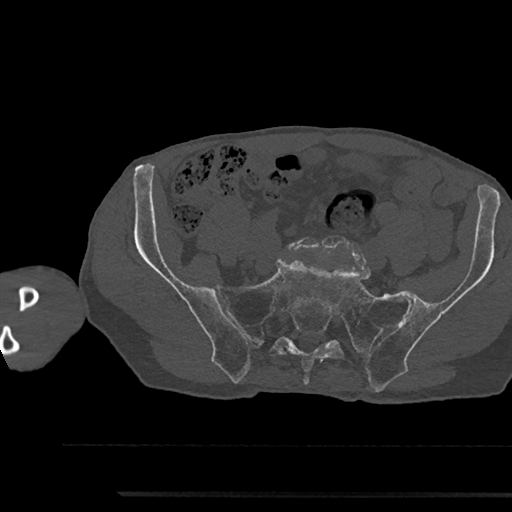
CT including the spine, one axial slice; slice 282 of 797 in the series (ordered by position); reconstruction kernel Br40s/3; 120 kVp; bone window (W 1800 / L 400 HU); 0.5 mm slice thickness; 512 × 512 image matrix. Patient: male, 79 years. Case-level facts recorded for this patient, not image findings: primary cancer: prostate.
Structures marked on this image (semi-automatically segmented with operator editing):
- L5 vertebra: bounding box [x1, y1, x2, y2] px = [287, 237, 318, 251]